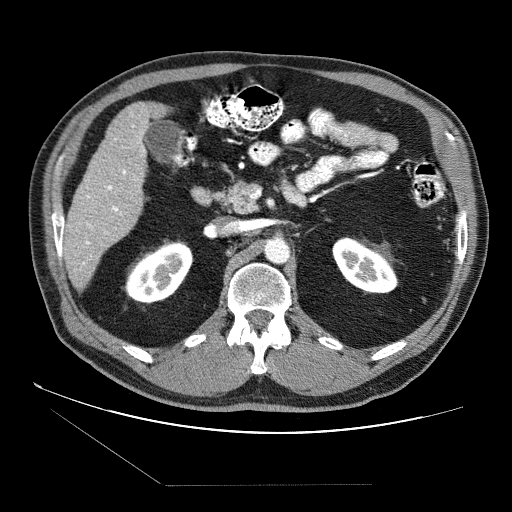
Contrast-enhanced abdominal CT (liver protocol), one axial slice. Slice 26 of 87 in the series (ordered by position). 120 kVp. Soft-tissue window (W 400 / L 40 HU). 512 × 512 image matrix, field of view 400 × 400 mm. From the clinical record (not read from this slice): diagnosis: hepatocellular carcinoma (patient treated with transarterial chemoembolisation; whether this scan precedes or follows treatment is not stated here); TNM stage (as recorded): Stage-II; Child-Pugh class: B; tumour differentiation: no biopsy; tumour nodularity: multinodular.
Annotated regions visible in this slice (semi-automatically segmented with operator editing):
- liver parenchyma outside the tumour (the mass and vessels are separate outlines, so this box may not span the whole liver): bounding box [x1, y1, x2, y2] px = [64, 102, 164, 289]
- liver vessels: [82, 126, 145, 265]